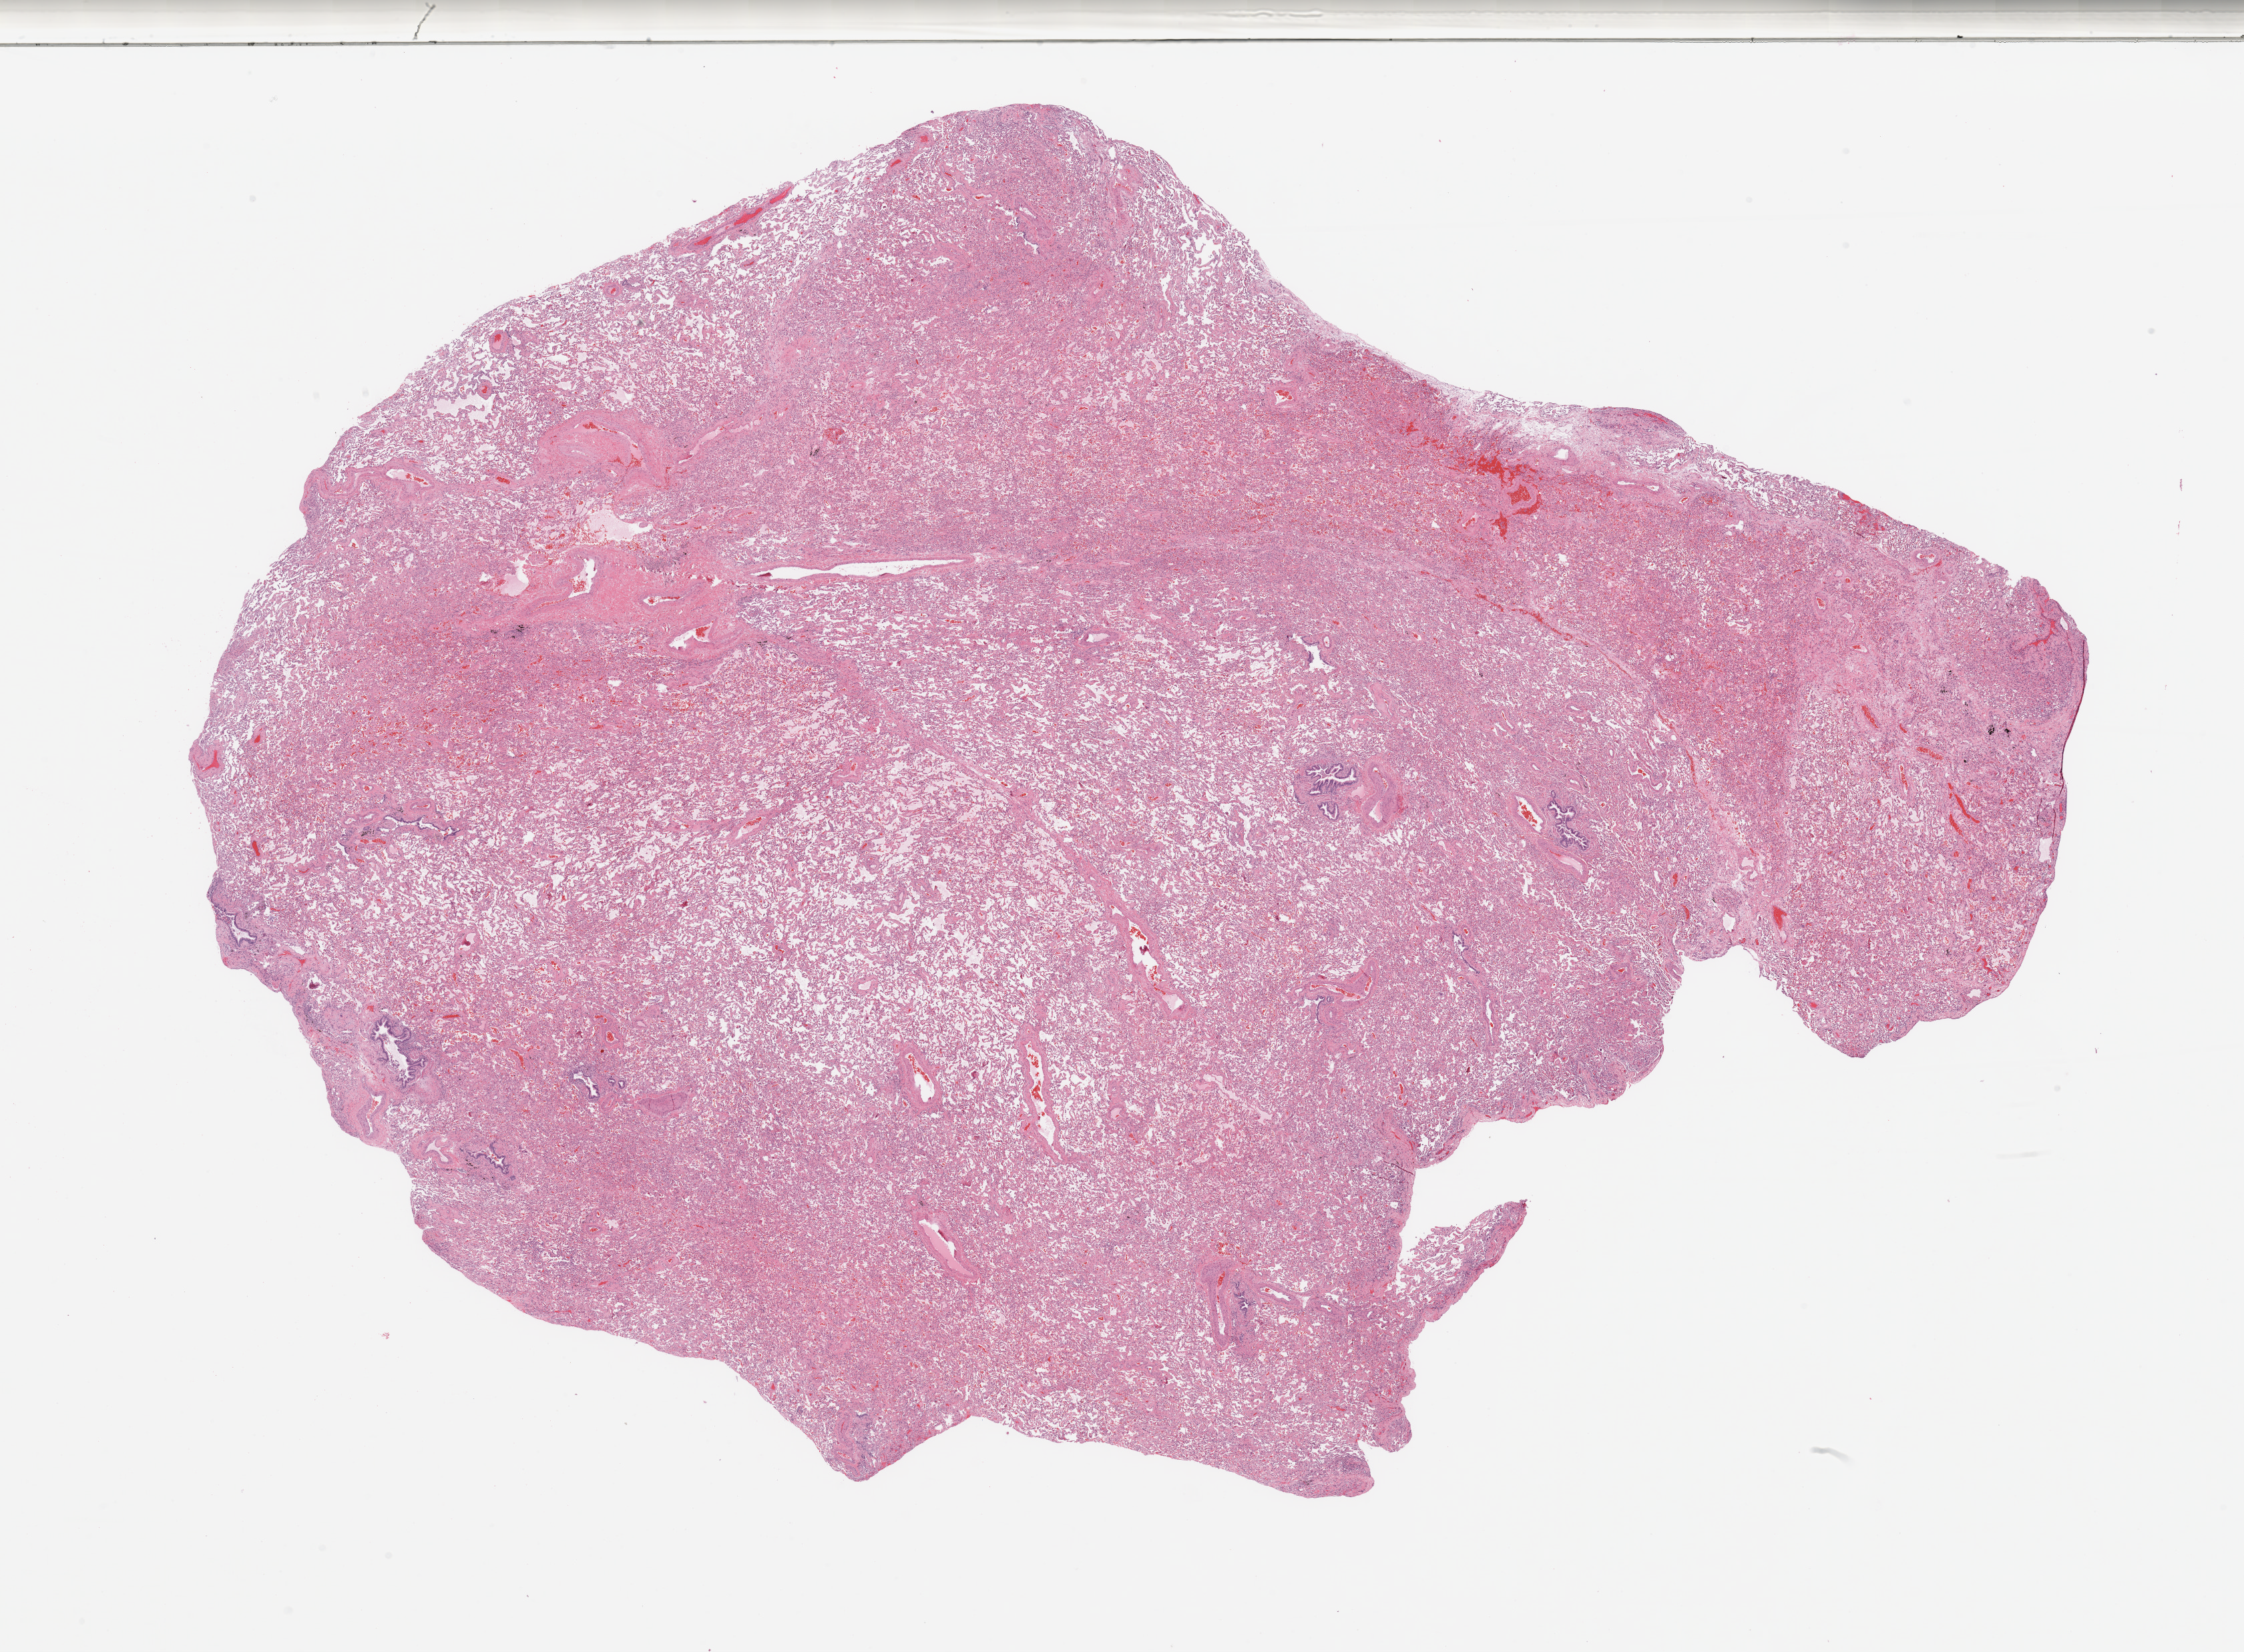
Whole-slide histology image, H&E-stained, whole scanned area (about 26.6 x 19.6 mm) shown as a low-resolution overview. Normal (non-tumour) tissue sample, sampled site: lung. Female, 62 y/o.
• this section: normal (non-tumour) tissue from the same patient
• patient diagnosis: Adenocarcinoma, NOS